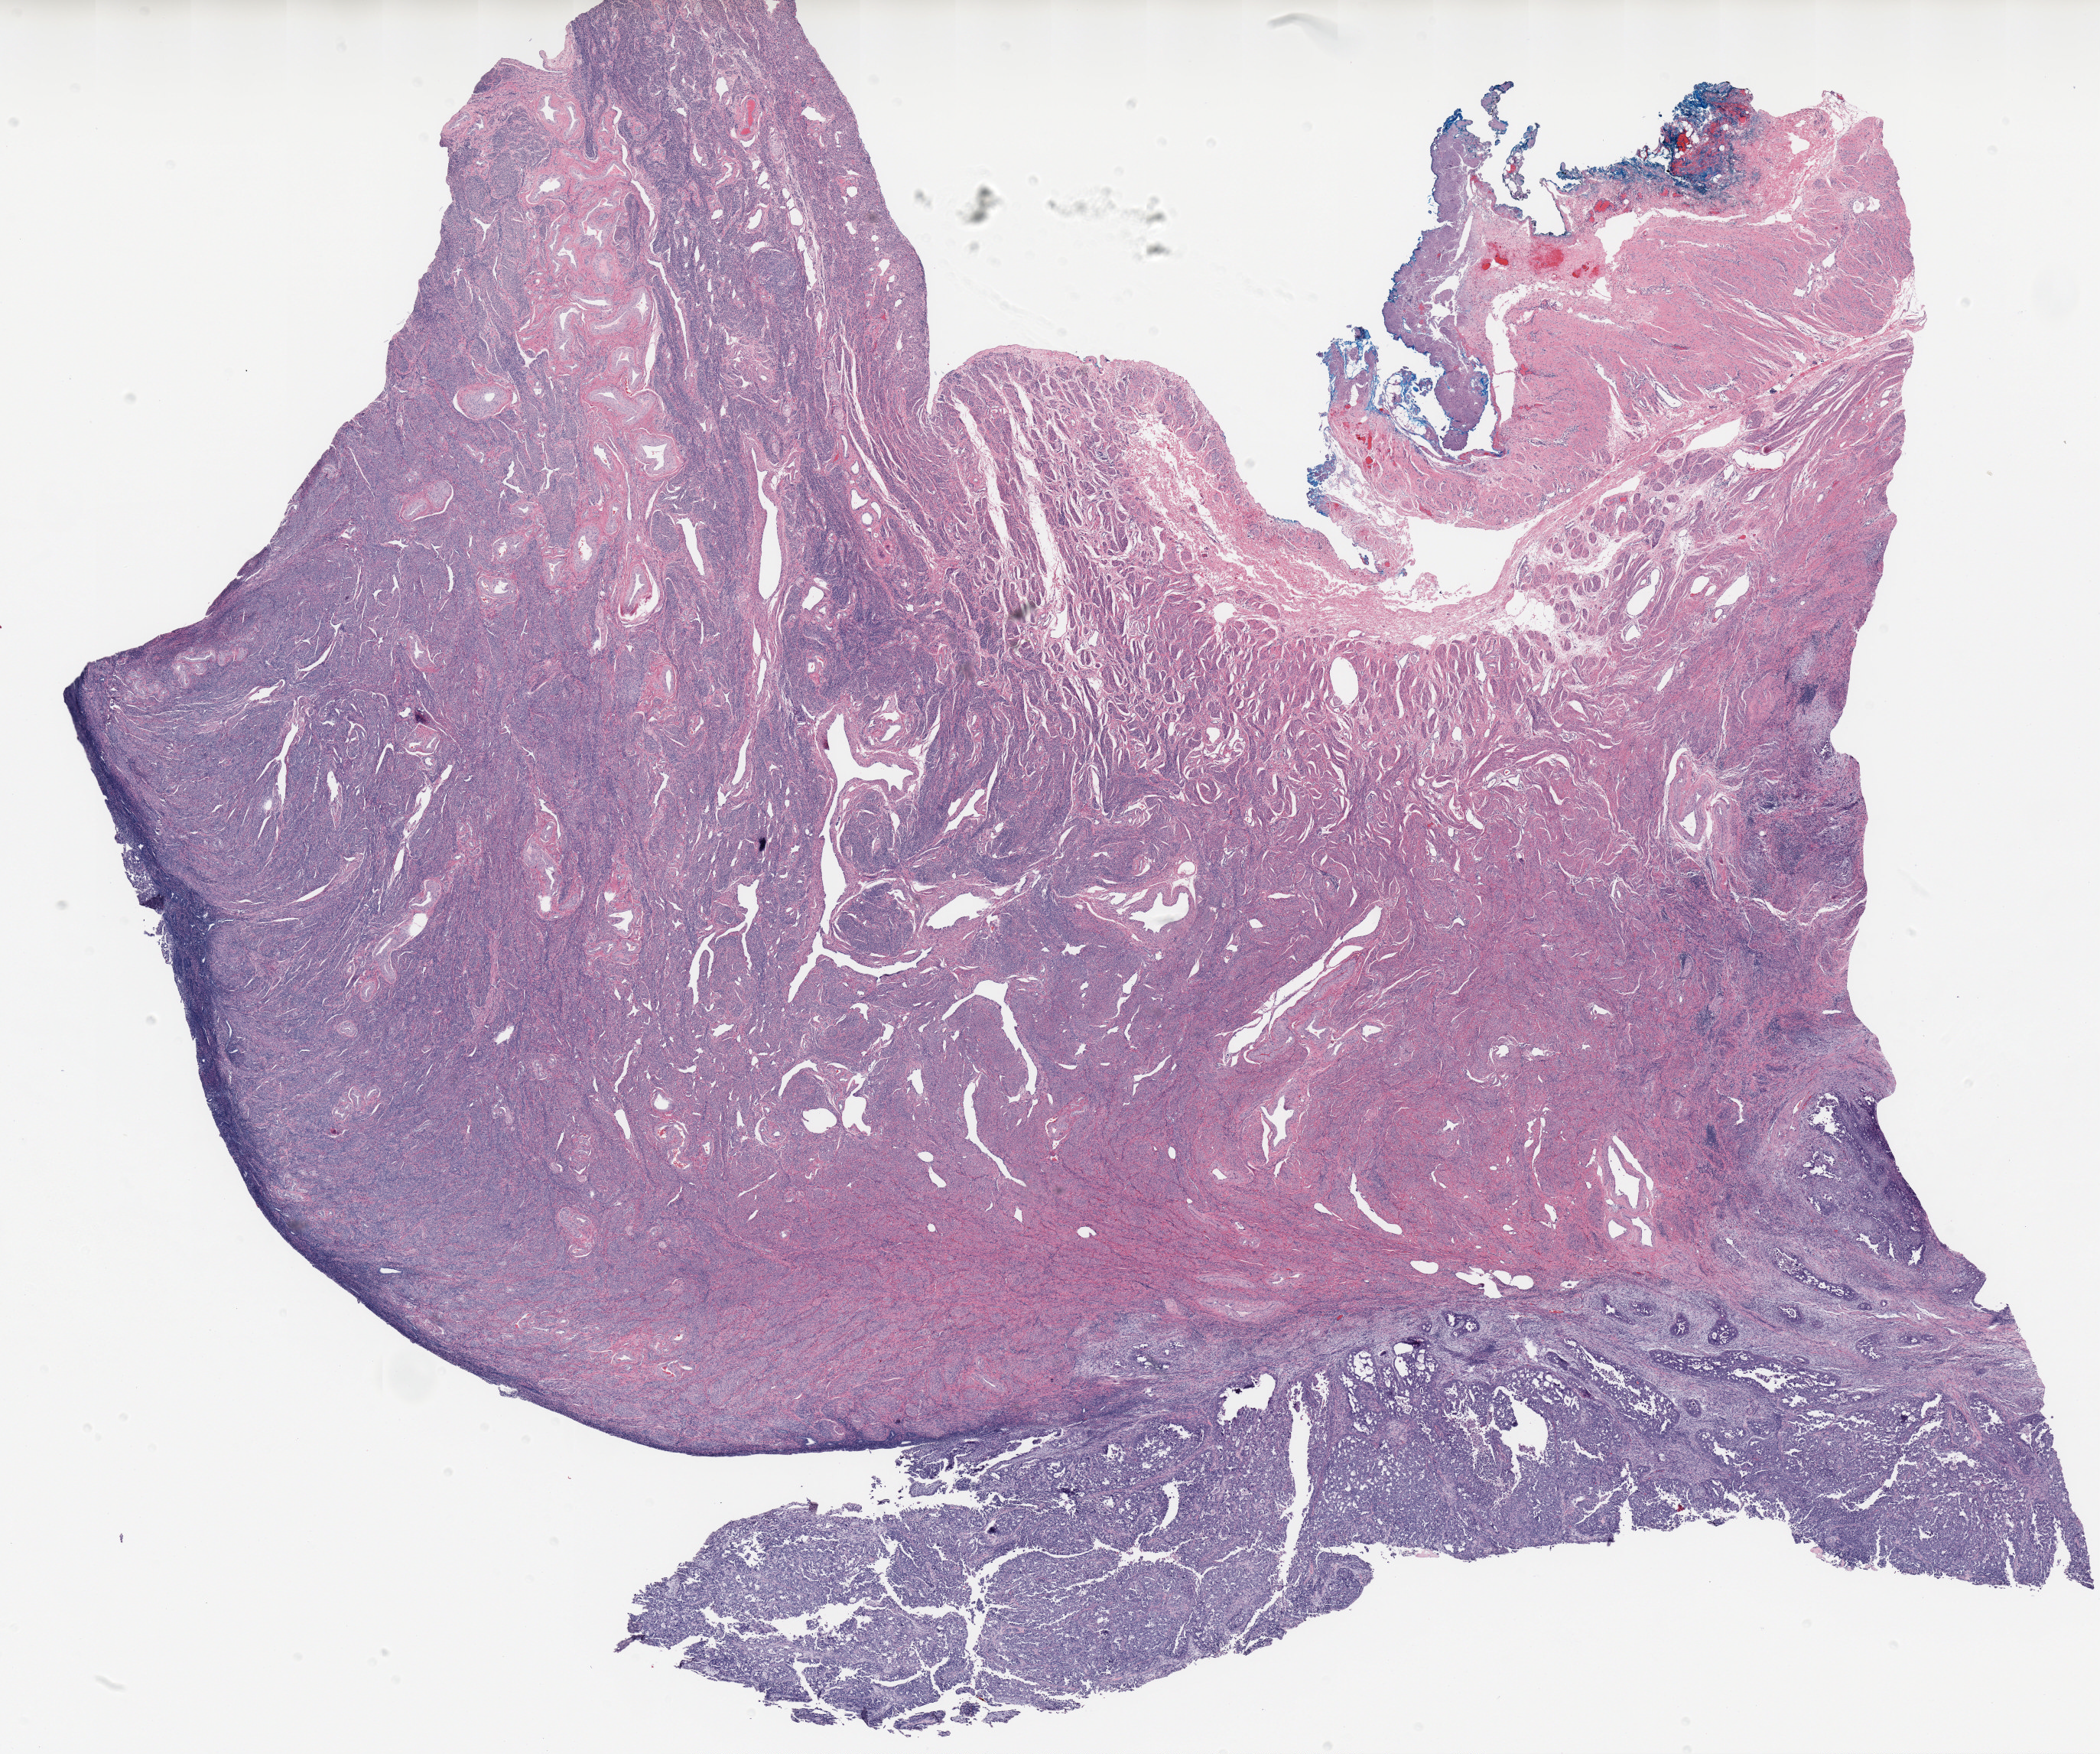
H&E-stained whole-slide image, low-resolution overview of the scanned area, about 21.9 x 18.3 mm, formalin-fixed paraffin-embedded (FFPE) diagnostic section, uterus, primary tumour sample. Female patient; age at initial diagnosis 56 years. Histologic grade: high grade.
Lymph nodes positive (case pathology): 12 of 29 examined. Diagnosis: Serous cystadenocarcinoma, NOS (endometrium). FIGO stage: IVB.